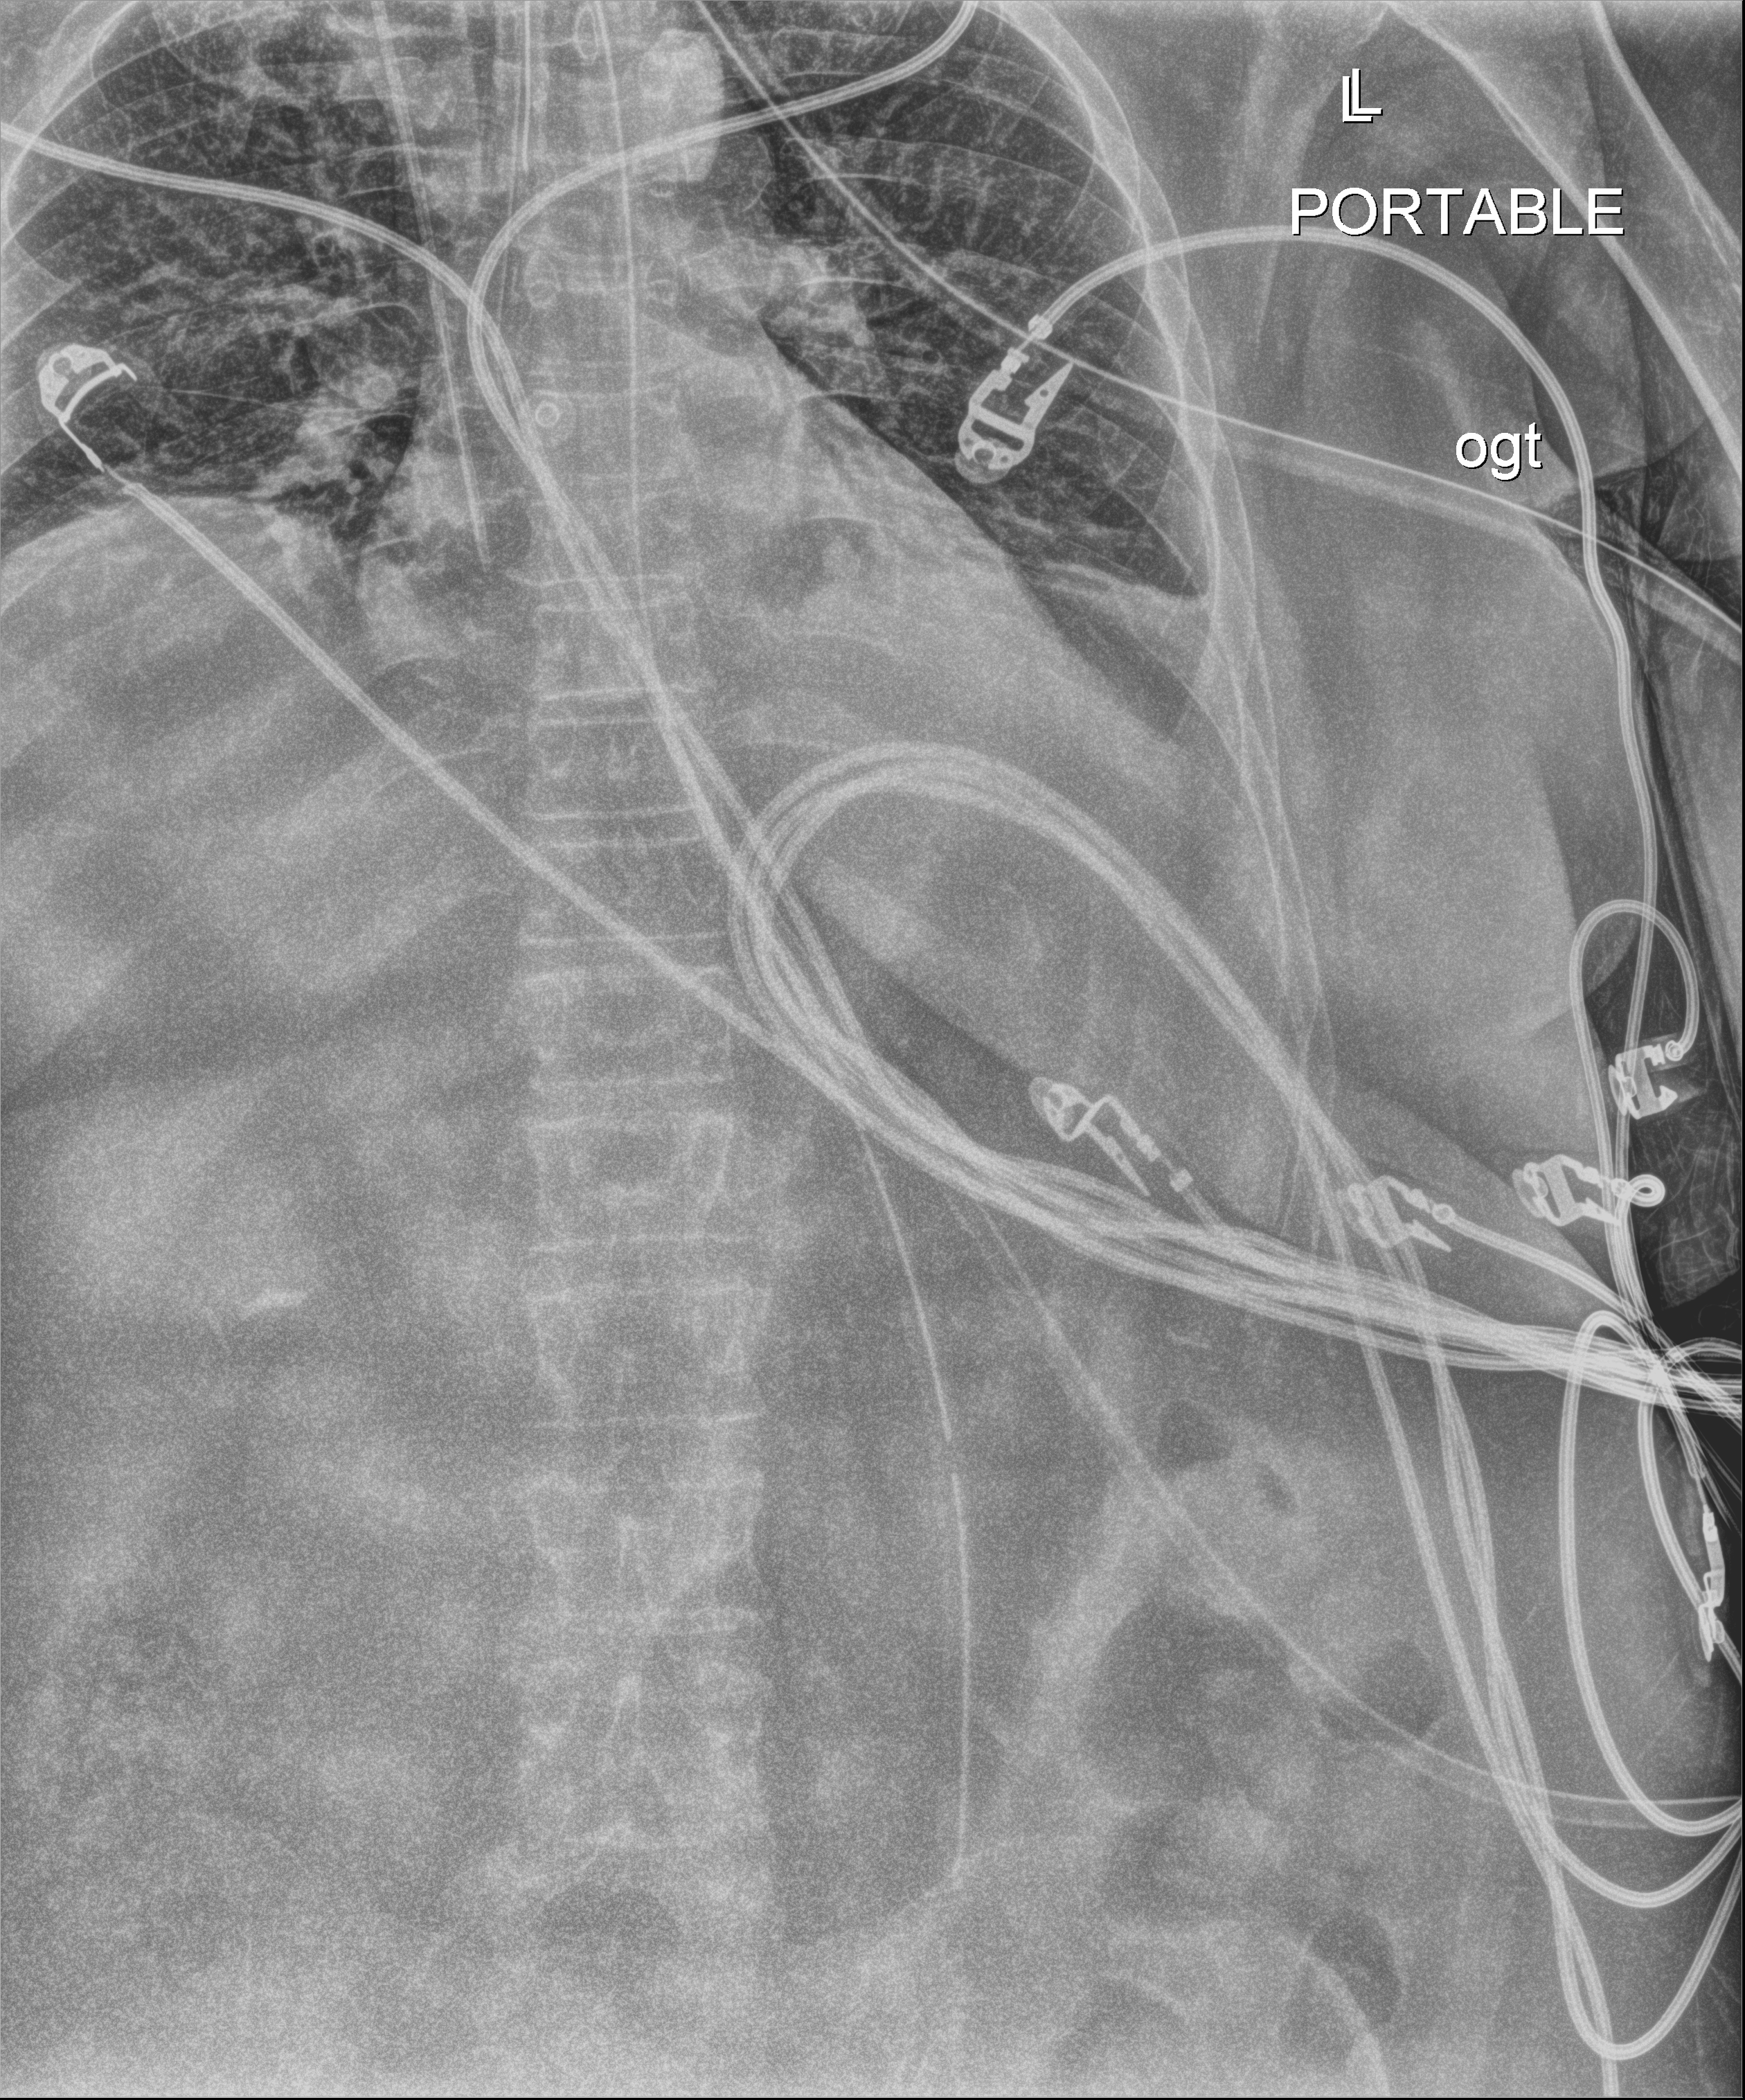
Bedside chest radiograph (digital radiography), anteroposterior (AP) projection. Patient hospitalised with COVID-19; female, aged 18–59 years.
From the hospital-stay record, not from the radiograph (when in the stay this image was taken is not recorded): mechanically ventilated during this hospital stay: no.